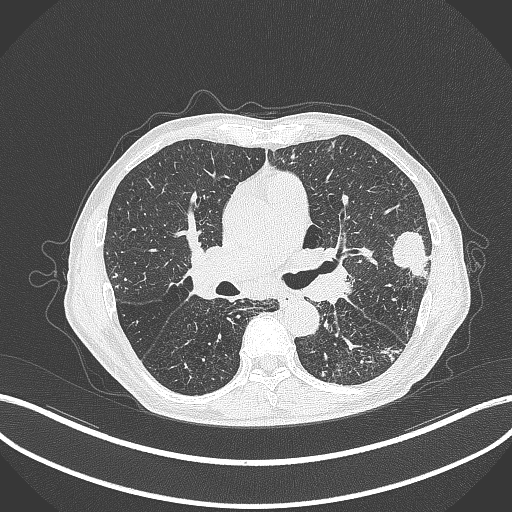
Chest CT, one axial slice. Position 236 of 463 along the scan axis. Lung window (W 1500 / L -600 HU). 1 mm slice thickness. 512 × 512 image matrix, field of view 400 × 400 mm. Male patient, age 74 years. From the clinical record (not read from this slice): clinical TNM (as recorded): T2a N1 M0.
Annotated regions visible in this slice (rectangle marked by the reading radiologist):
- lung tumour (recorded histology: adenocarcinoma): bounding box <387,227,431,282> (left, top, right, bottom; pixels)